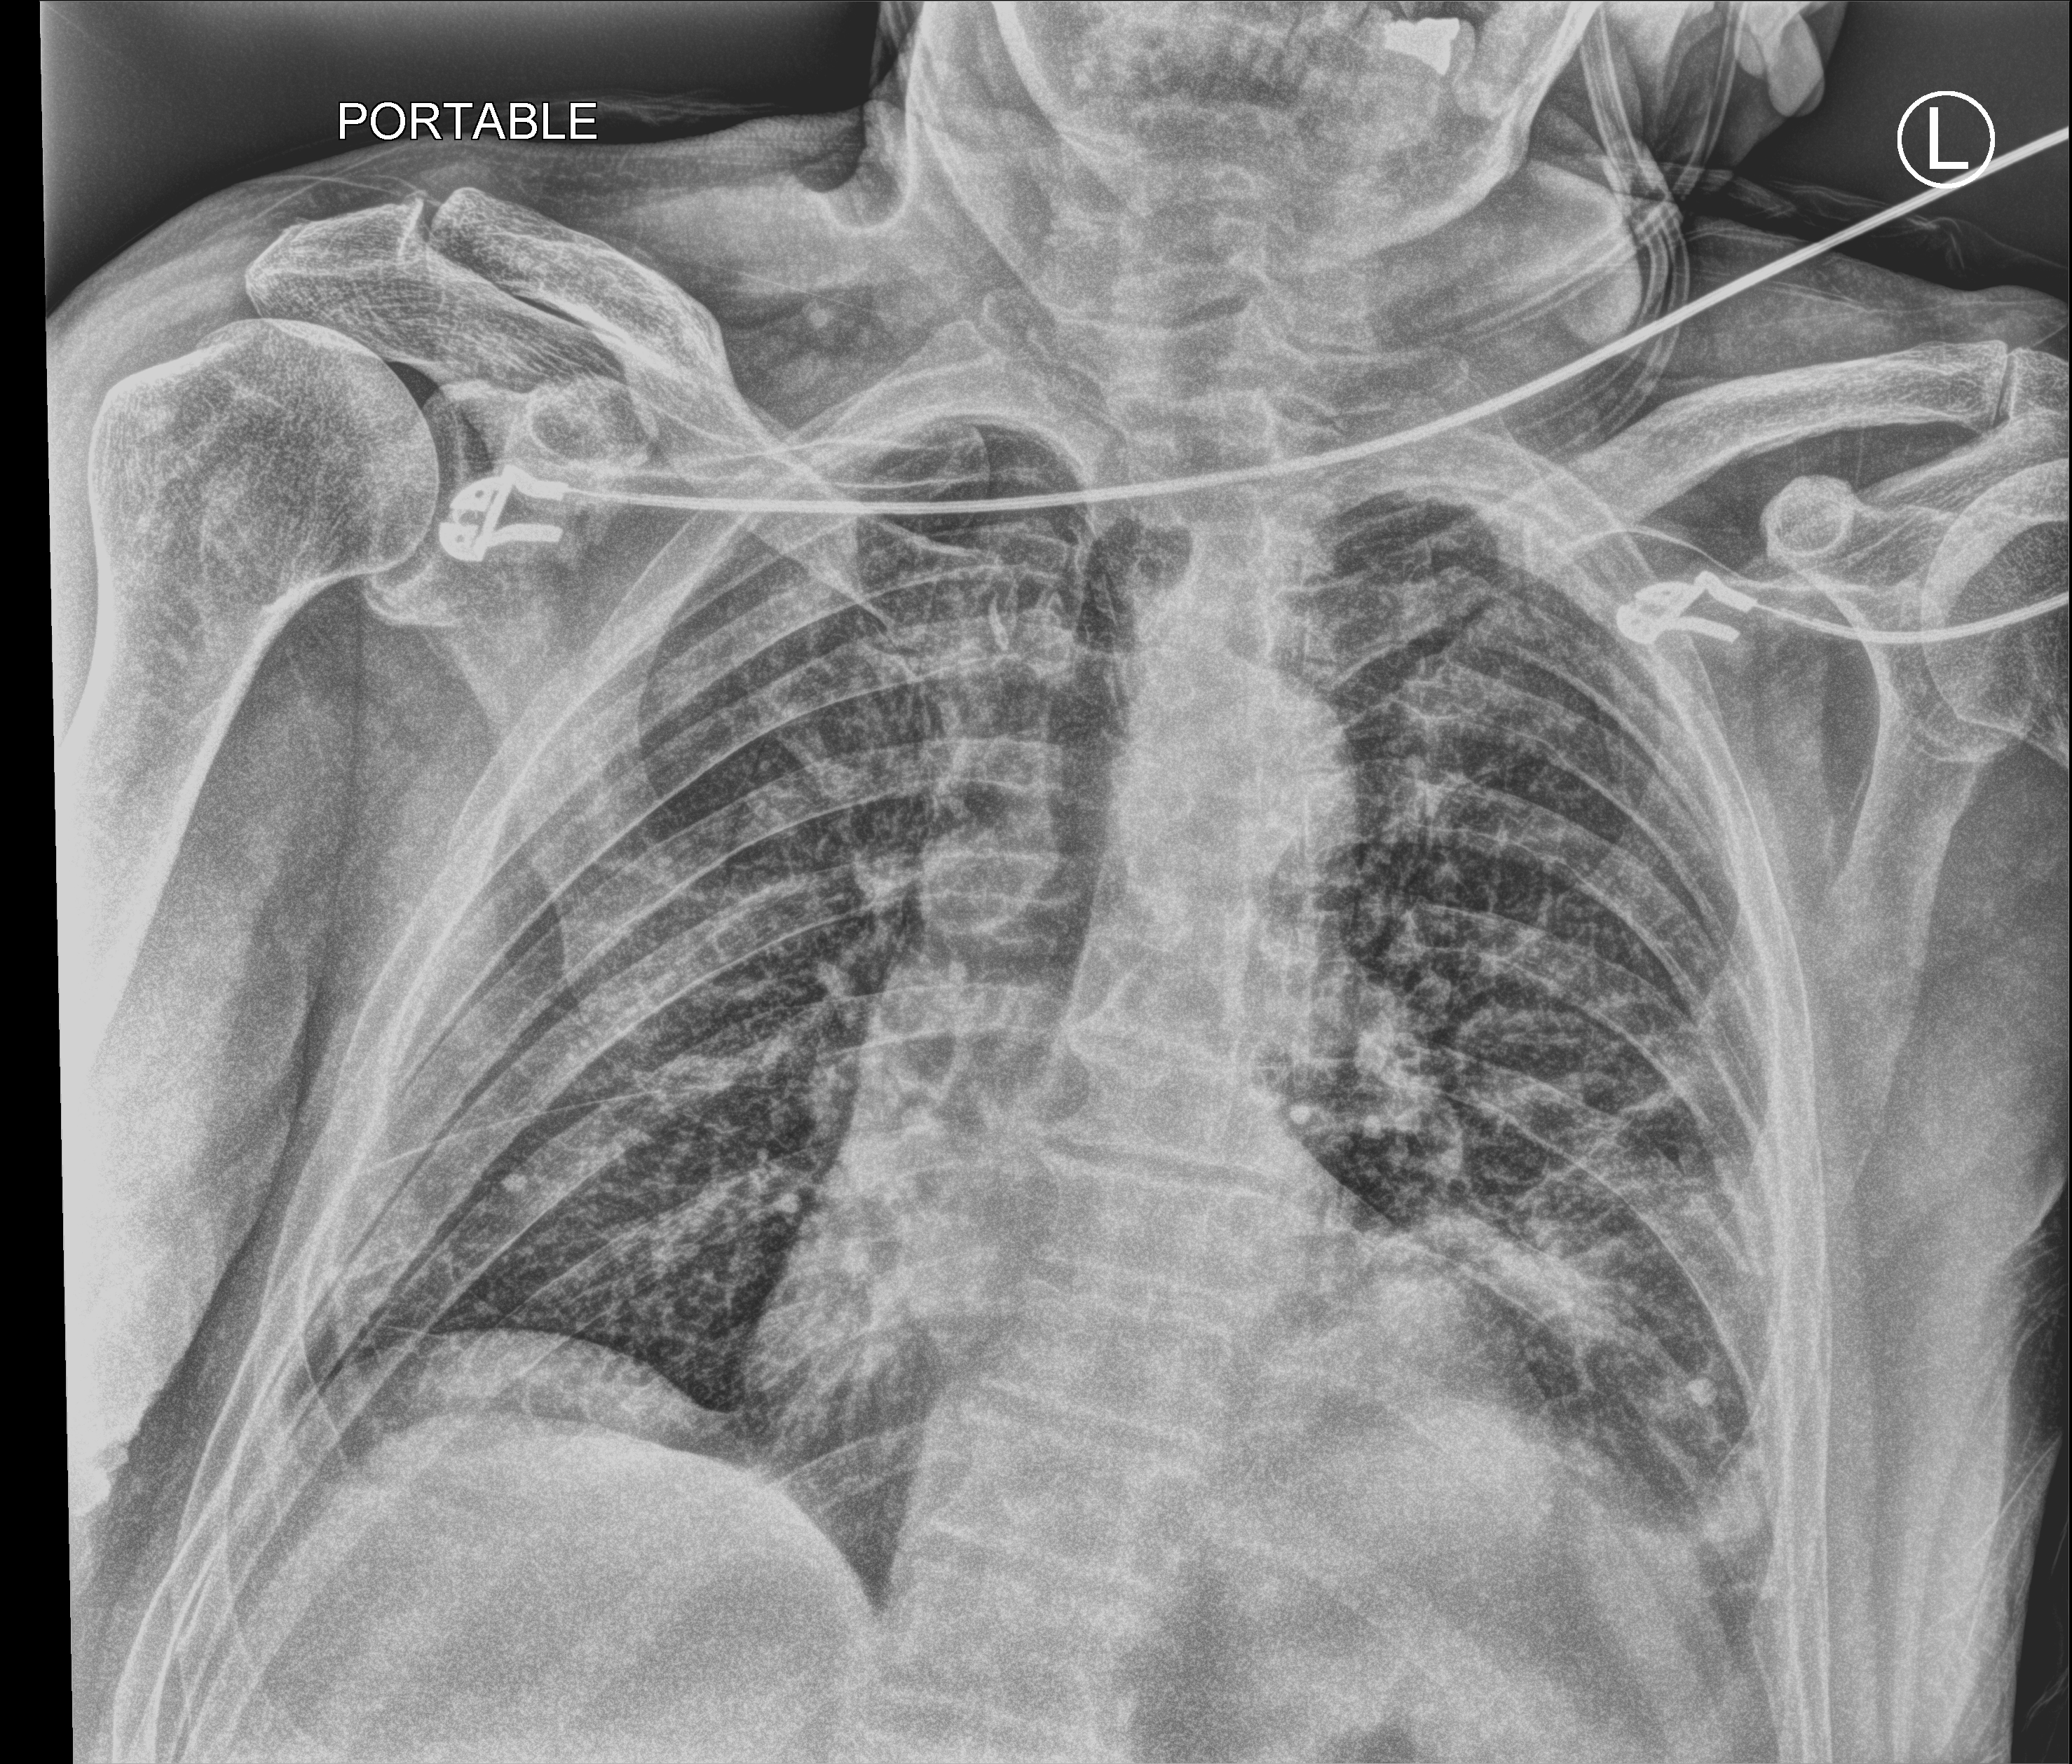
Portable chest radiograph. Patient hospitalised with COVID-19; male, aged 75–90 years.
Admission-level facts for this patient (not findings on this image; timing relative to this image not recorded):
- chronic kidney disease (admission record): yes
- diabetes (admission record): no